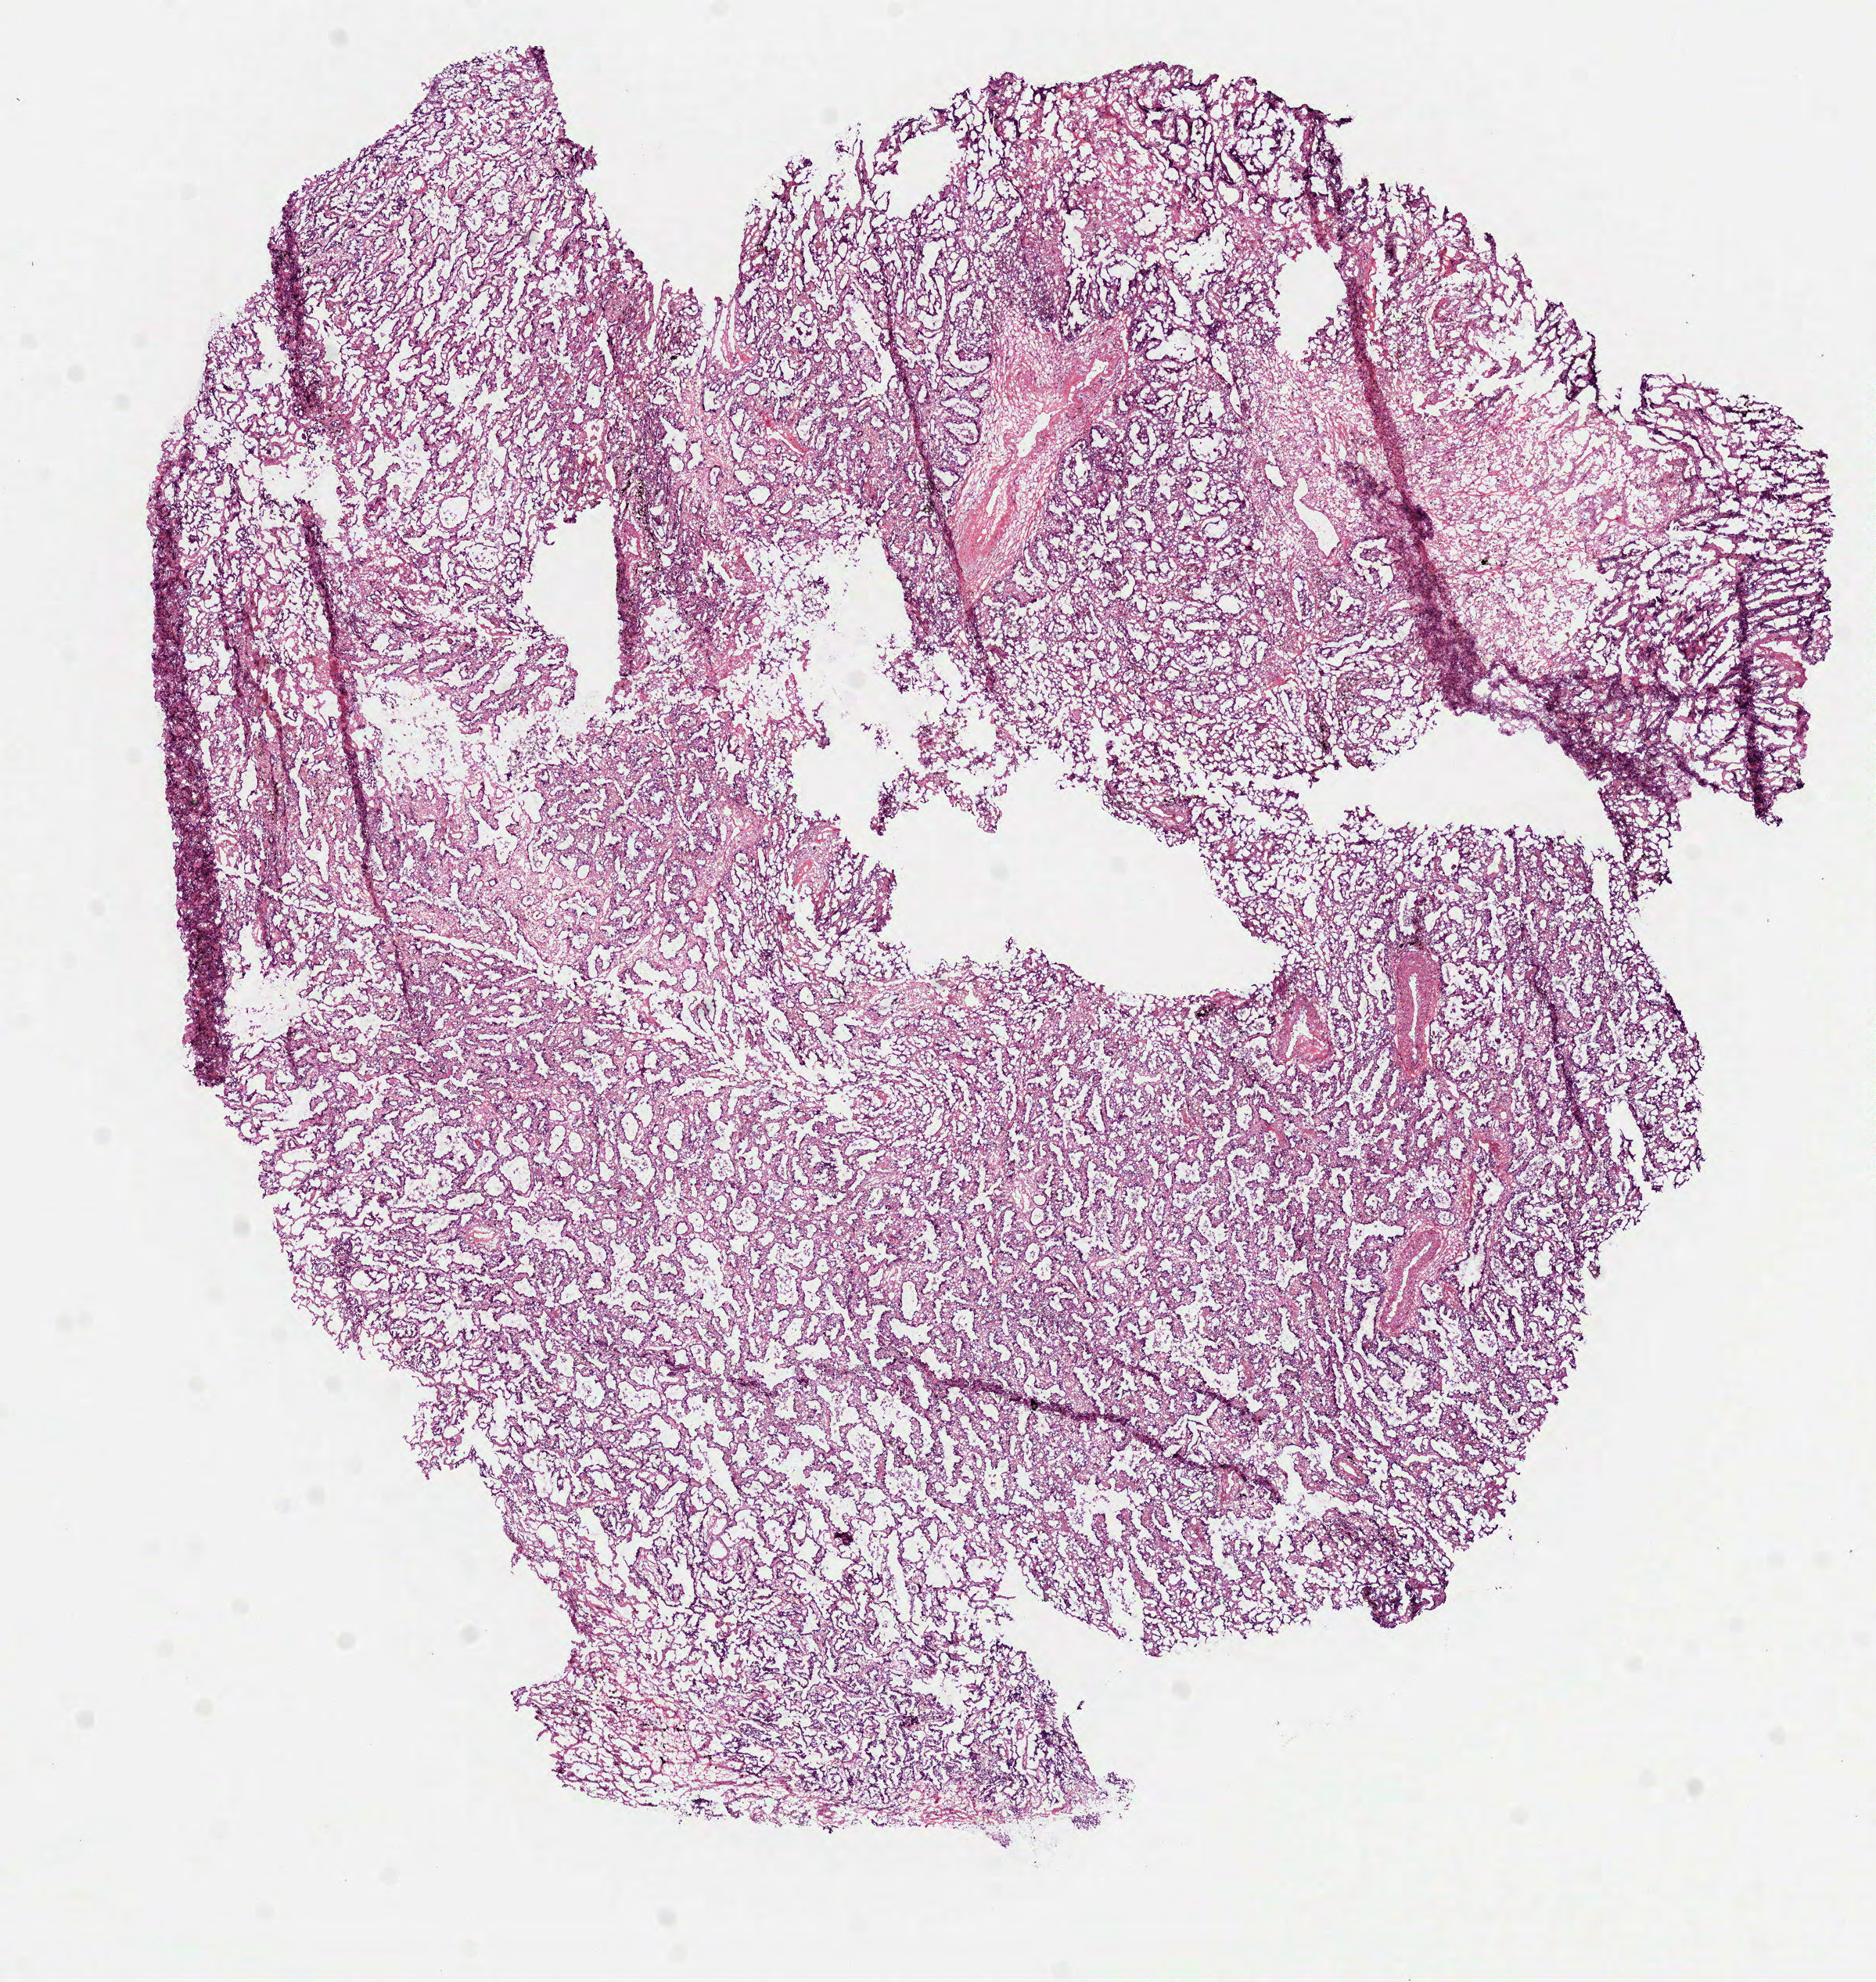
Hematoxylin and eosin (H&E) stained whole-slide image, low-resolution overview of the scanned area, about 9.7 x 10.2 mm, frozen section from the bottom of the tissue portion, sample: primary tumour, lung. Patient: female, age at initial diagnosis 67 years. Pathologist review of this section (percent, as recorded): tumour cells 83%, tumour nuclei 75%, normal cells 0%, stromal cells 12%, necrosis 5%.
Diagnosis: Adenocarcinoma, NOS (upper lobe, lung). AJCC pathologic stage: IIB (6th edition).